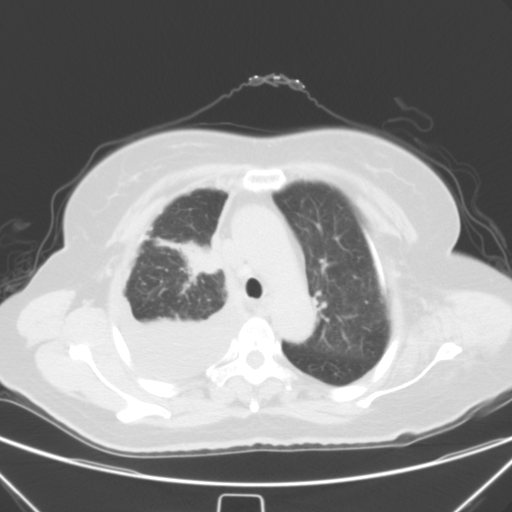
Chest CT, one axial slice; slice 42 of 55 in the series (ordered by position); lung window (W 1500 / L -600 HU); 512 × 512 image matrix. Female patient, age 66 years. From the clinical record (not read from this slice): clinical TNM (as recorded): T2 N0 M1.
Outlined on this slice (bounding box drawn by a radiologist):
- lung tumour (recorded histology: adenocarcinoma): box from (x=174, y=237) to (x=219, y=276) px